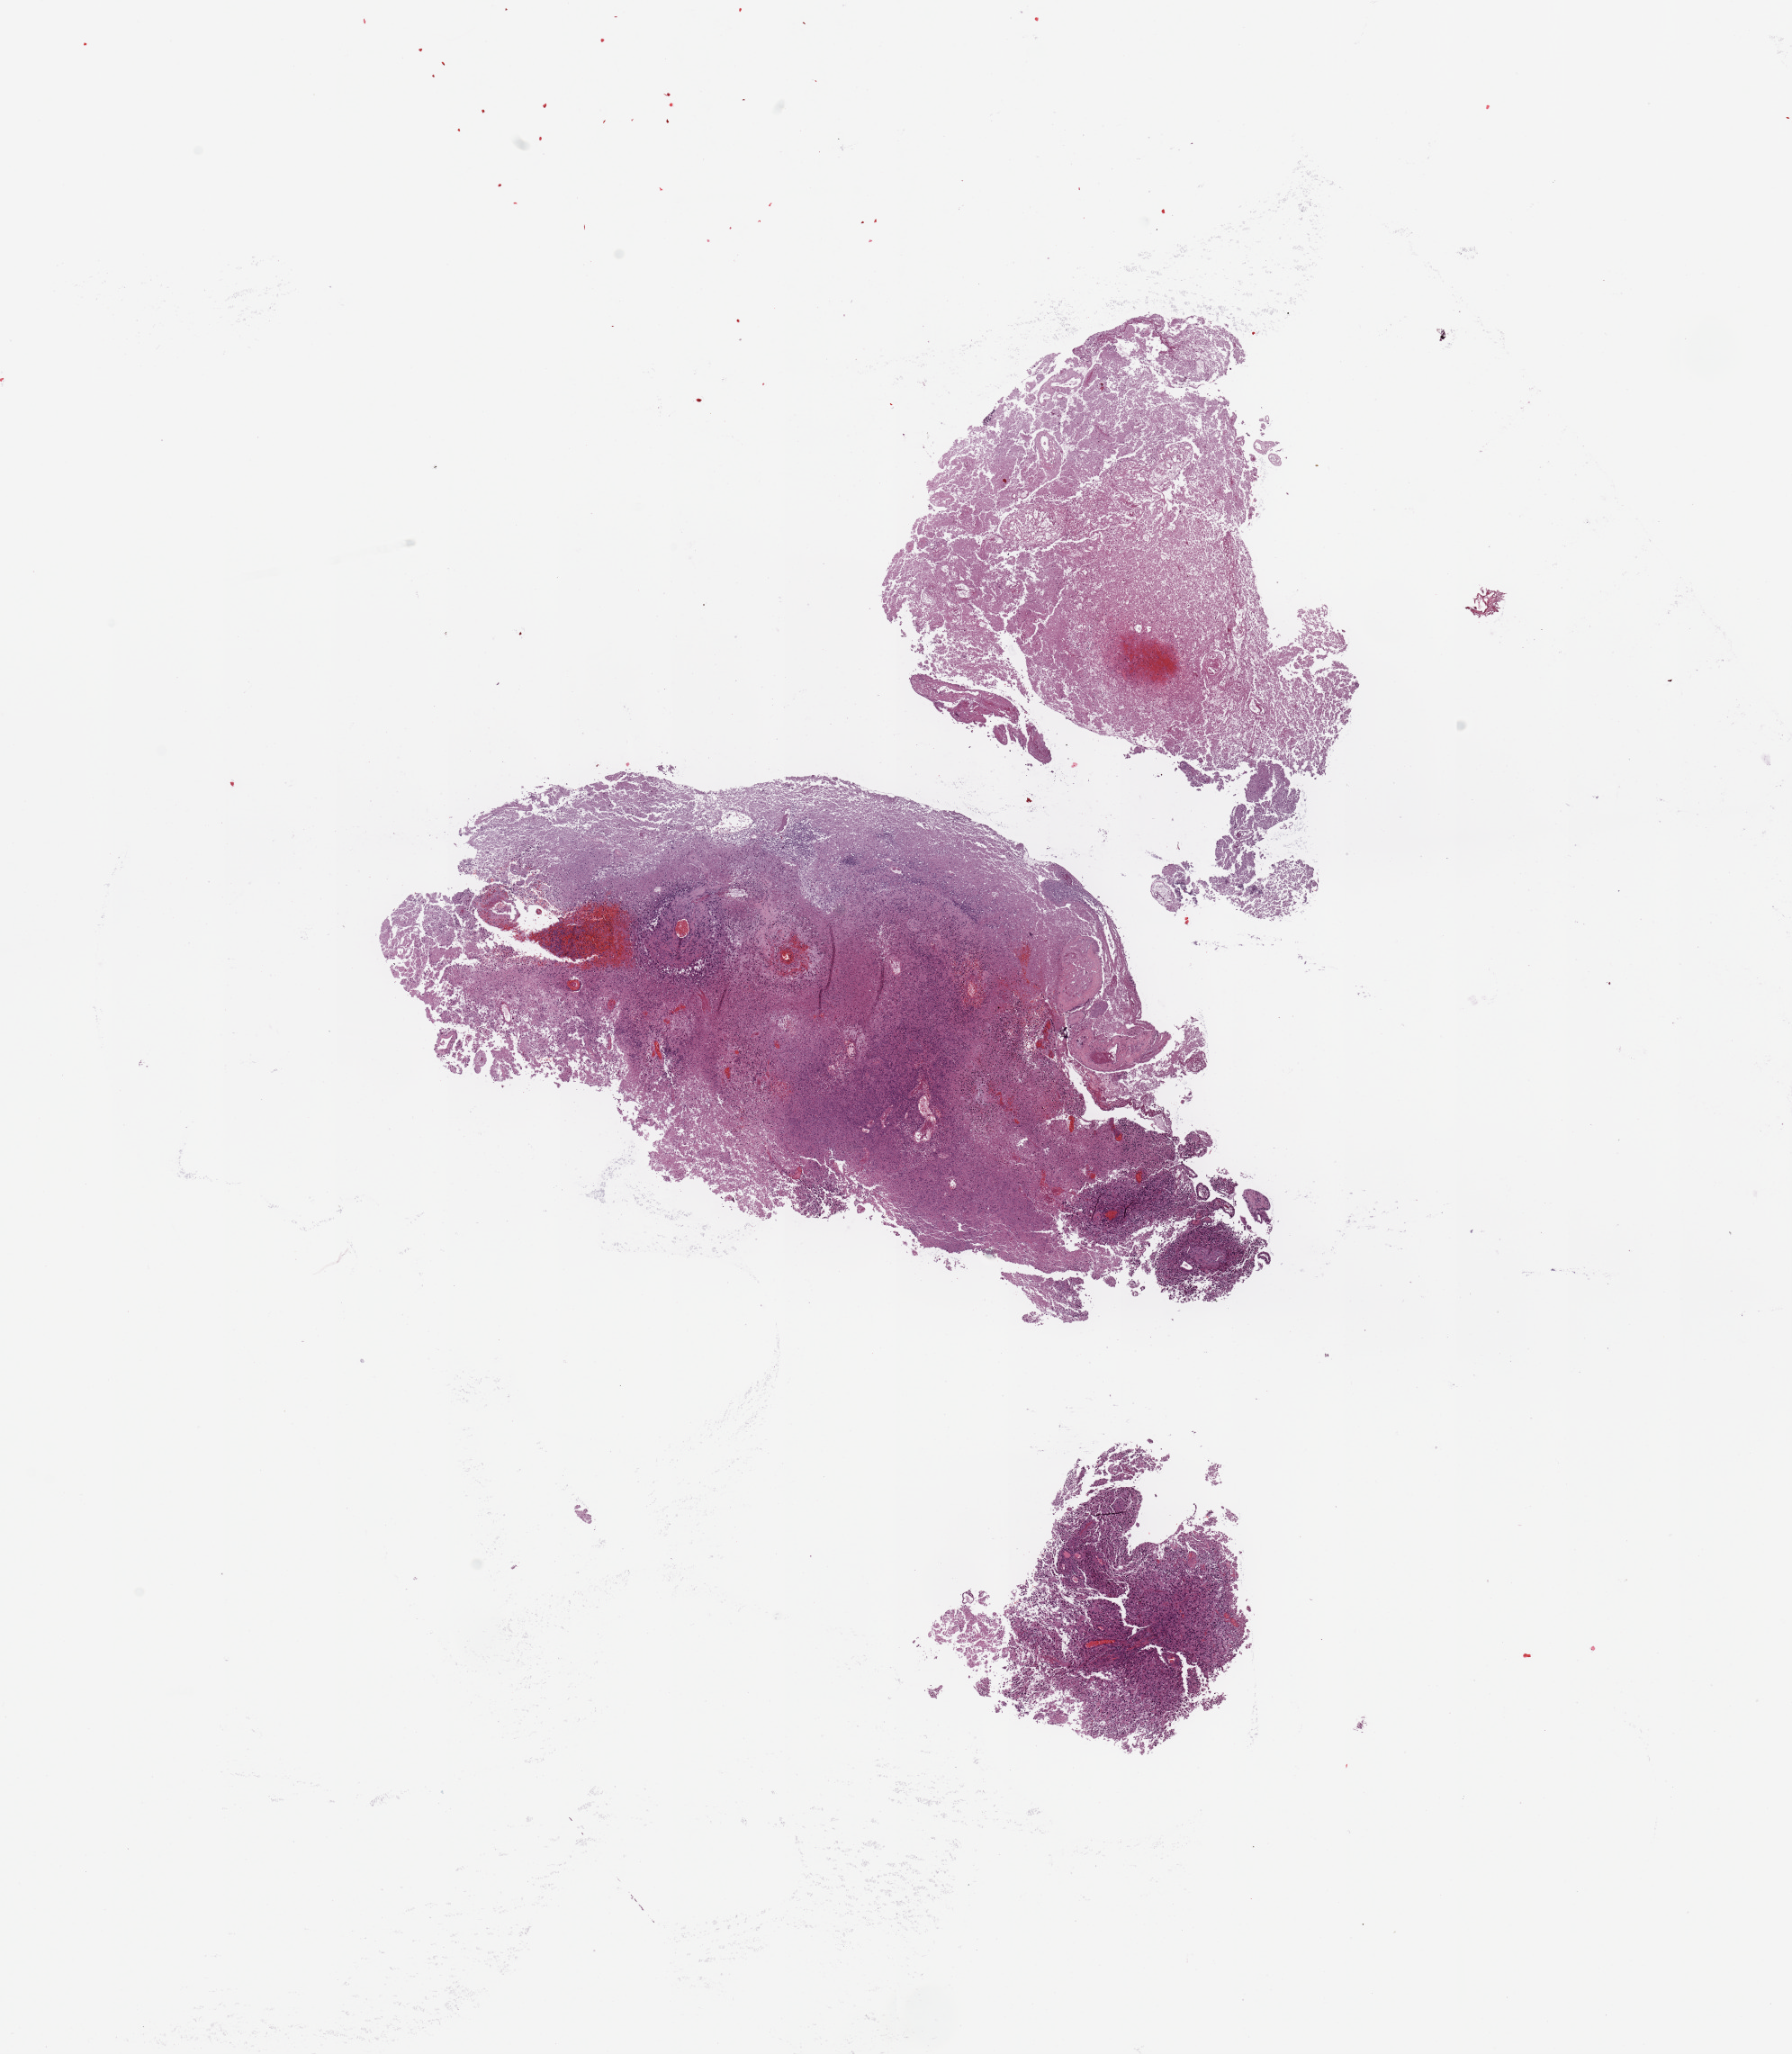
Whole-slide histology image, Hematoxylin and eosin (H&E) stained, low-resolution overview of the scanned area, about 15.8 x 18.1 mm, brain, tumour tissue. Patient: male, age 53 years.
- diagnosis: Glioblastoma
- primary tumour site (as recorded): frontal lobe